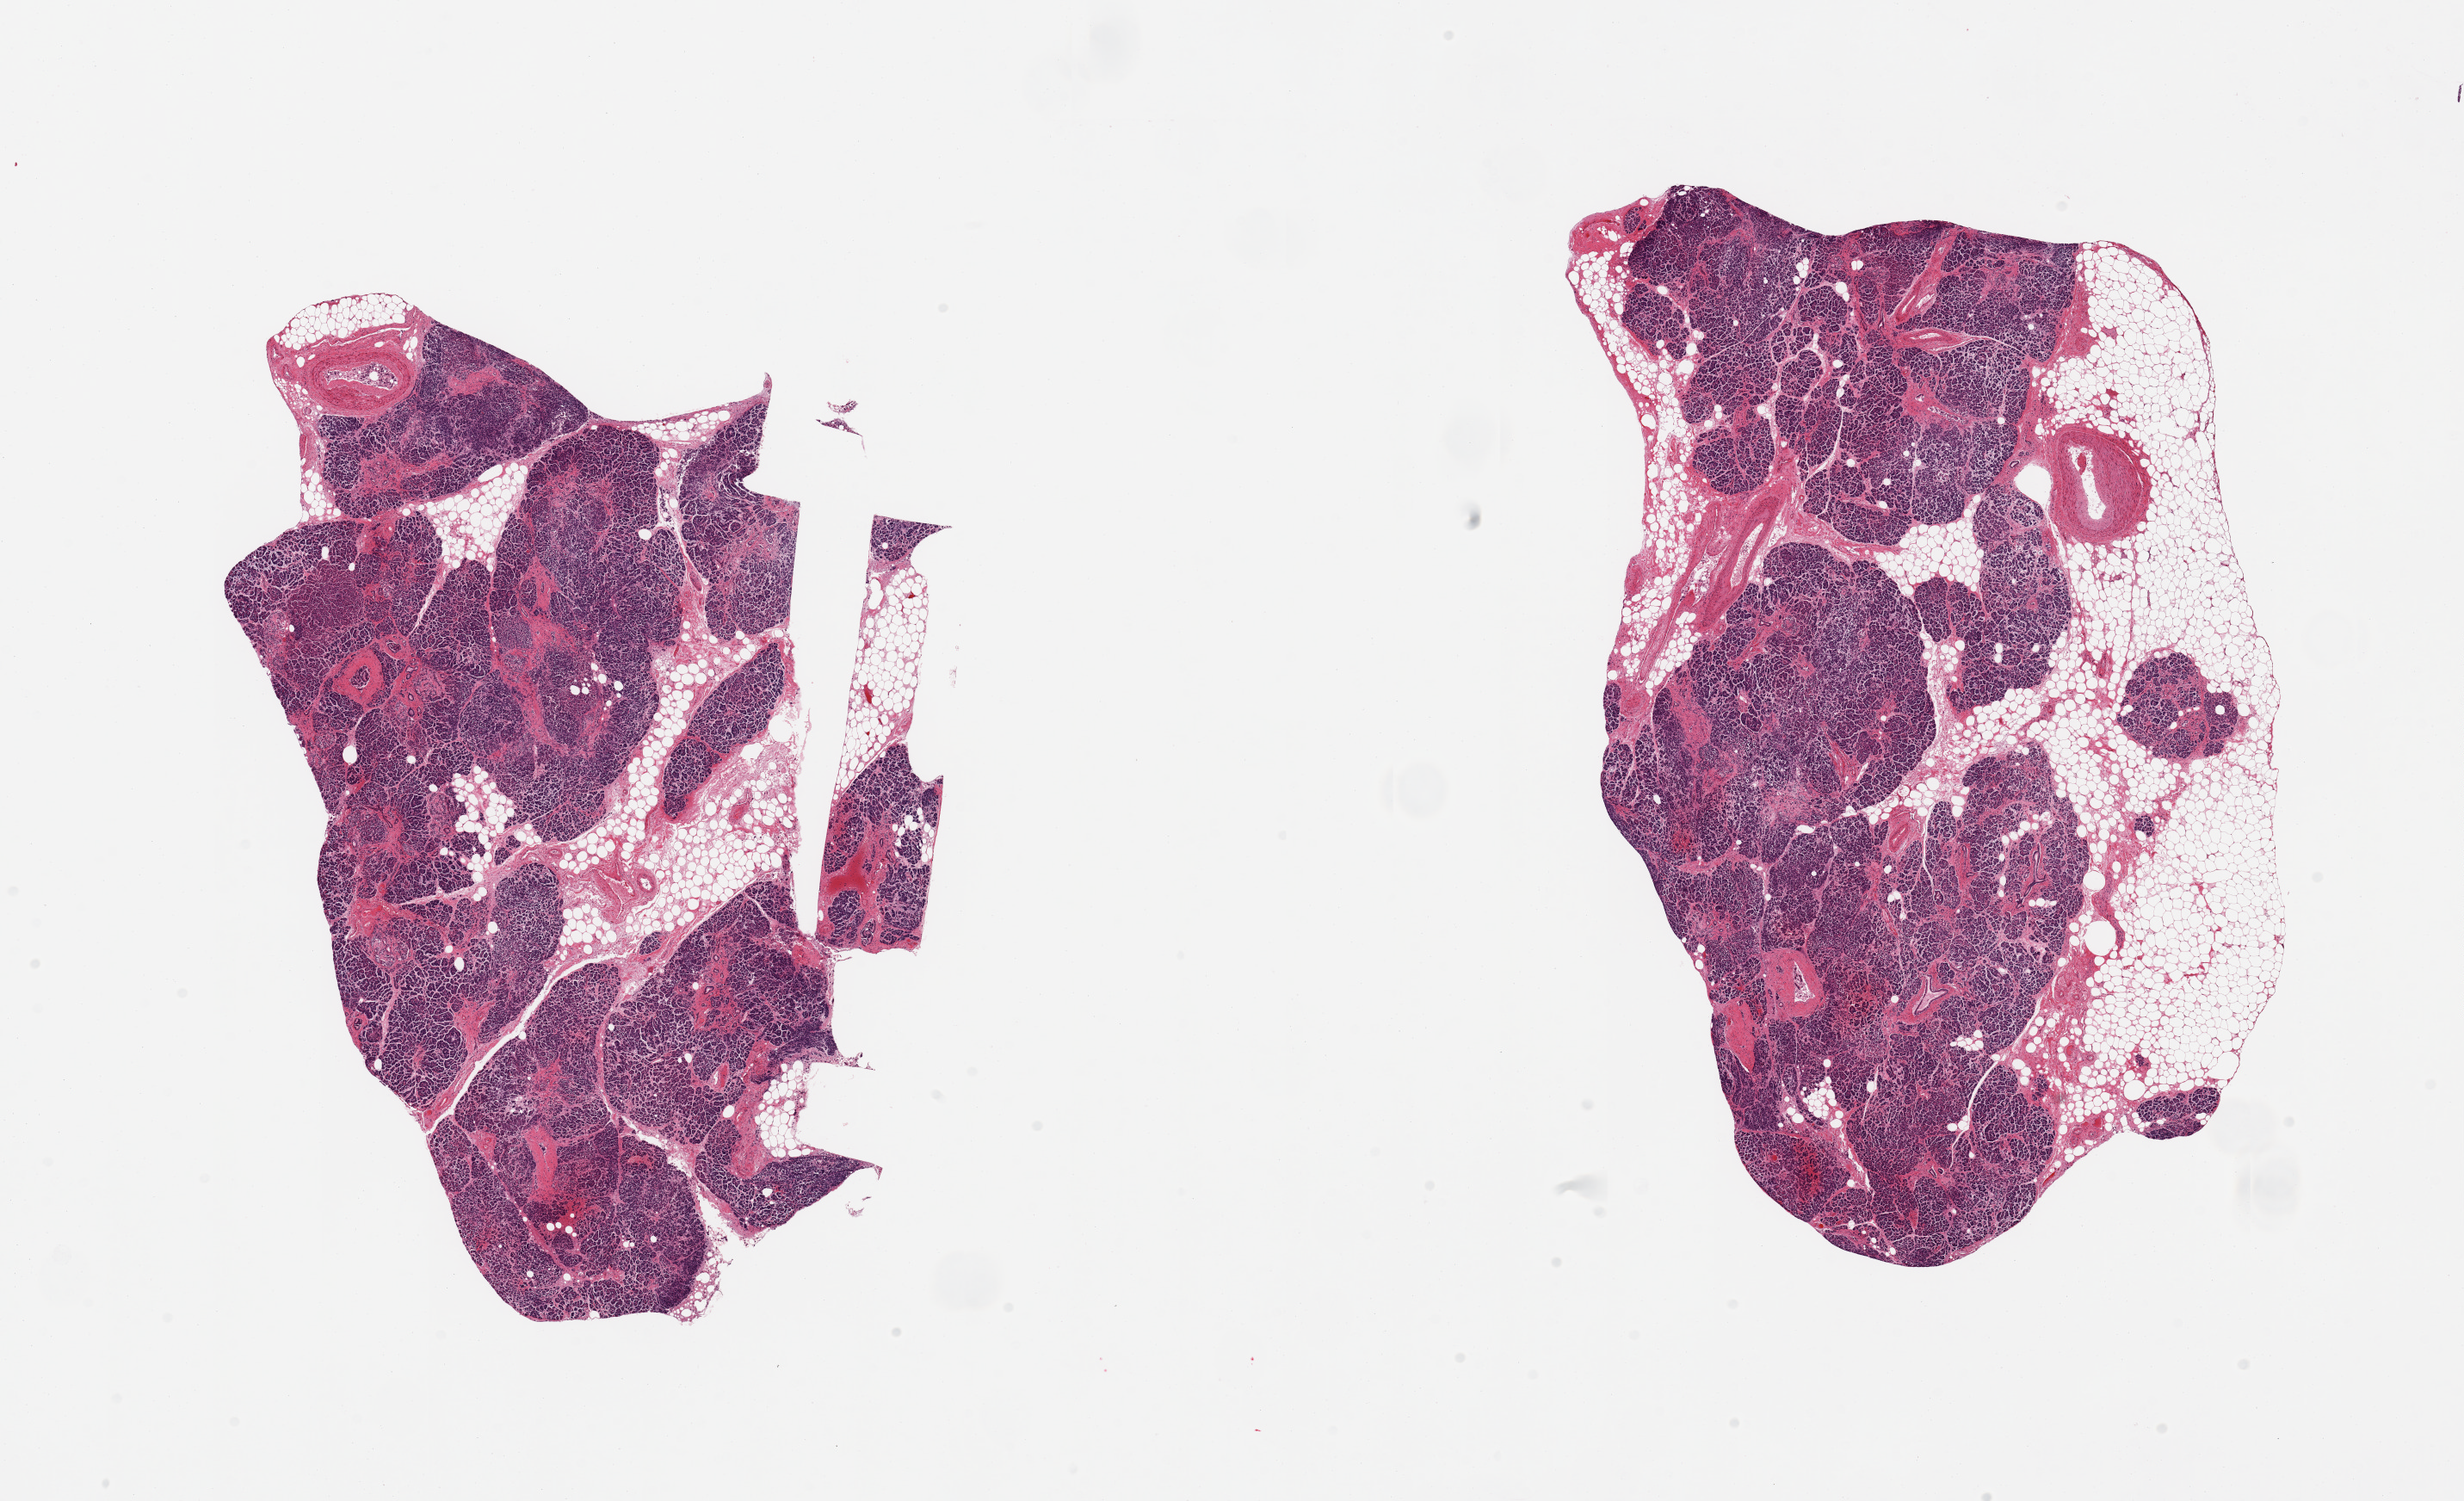
Digitized haematoxylin and eosin-stained section — whole scanned area (about 22.6 x 13.8 mm) shown as a low-resolution overview. PAXgene-fixed, paraffin-embedded tissue. Section of pancreas (target tissue). Tissue donor sample. Donor: male.
Review note (as recorded): 2 pieces, moderate saponification, islets degrading, fat is ~25% of specimen.